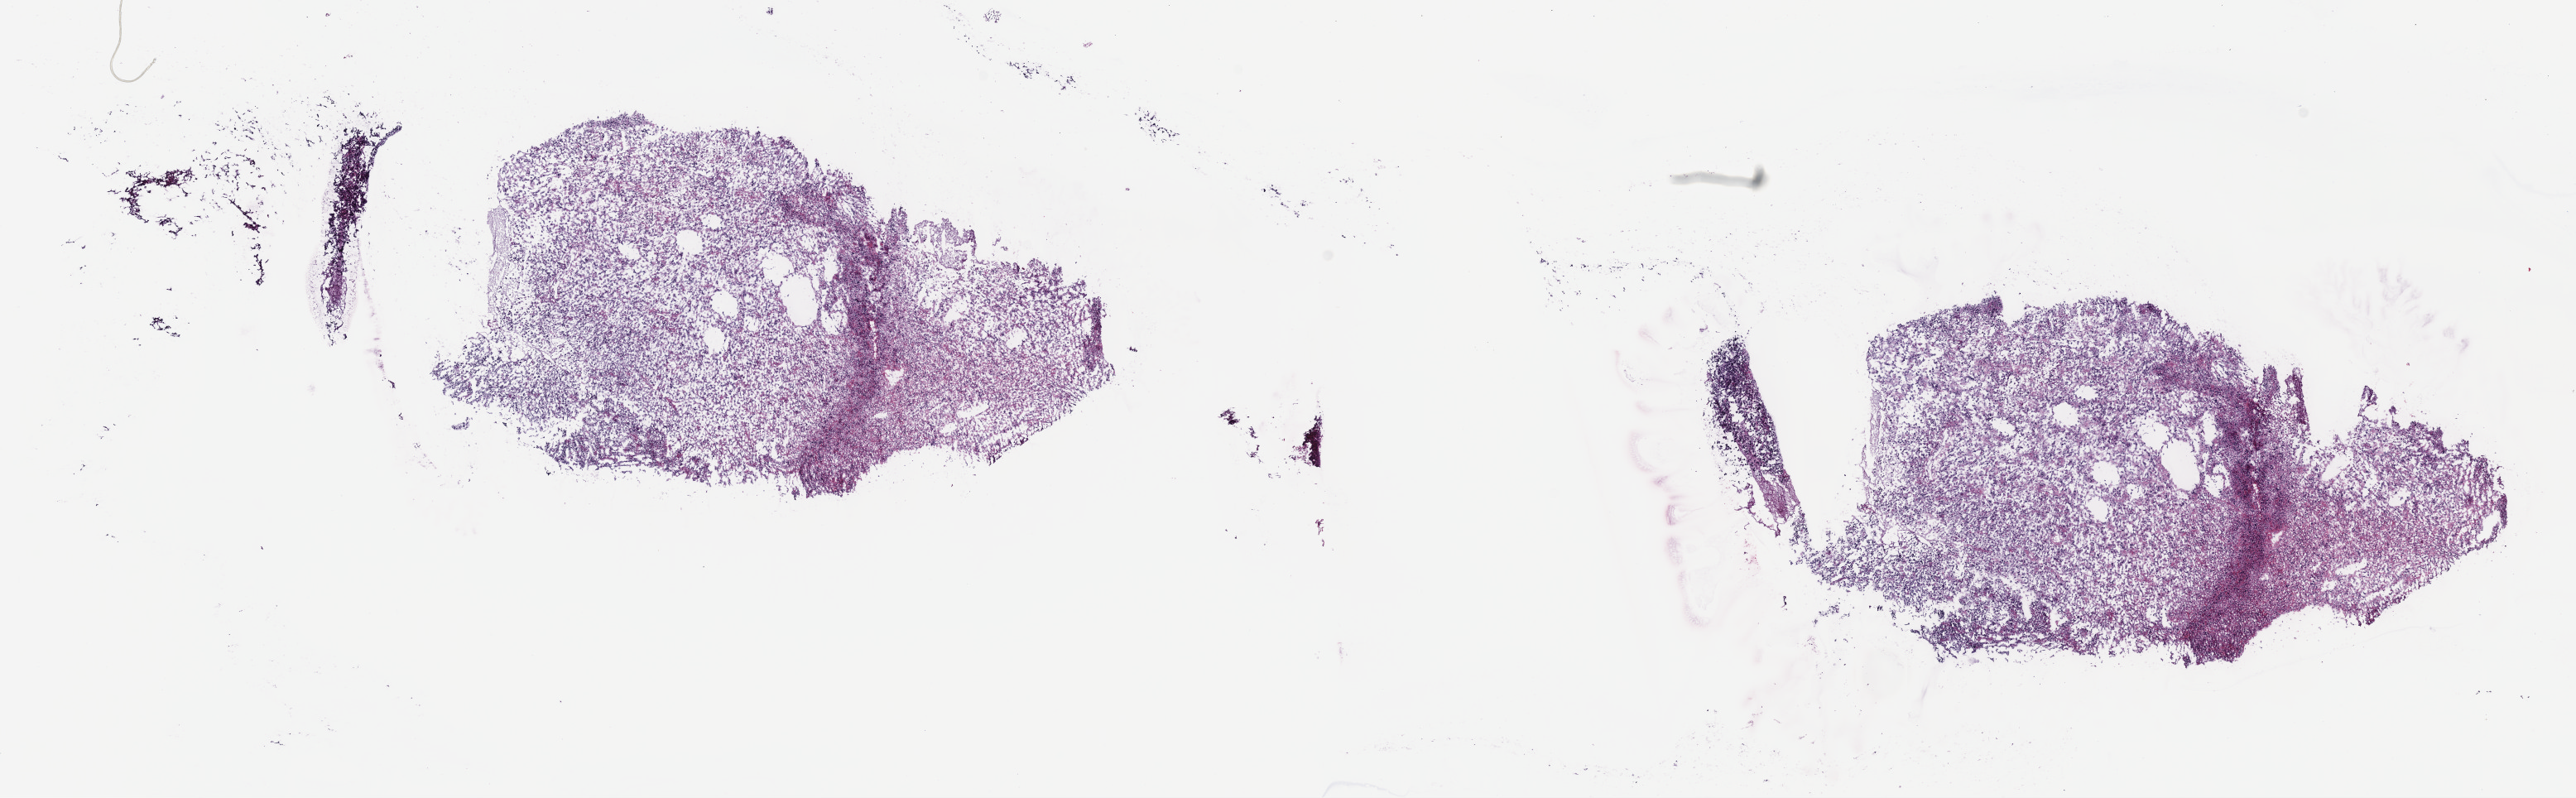
Digitized Hematoxylin and eosin (H&E) stained tissue section (whole slide) — low-resolution overview of the scanned area, about 25.2 x 7.8 mm (from a 40x scan); frozen section; sample: primary tumour, brain. Patient: female, age at initial diagnosis 54 years. Histologic grade: G3 (poorly differentiated). Pathologist review of this section (percent, as recorded): tumour cells 55%, tumour nuclei 90%, normal cells 10%, stromal cells 35%, necrosis 0%. Inflammatory infiltration, as recorded: lymphocyte infiltration 0%, monocyte infiltration 0%, neutrophil infiltration 0%.
Diagnosis: Astrocytoma, anaplastic. Laterality: left.